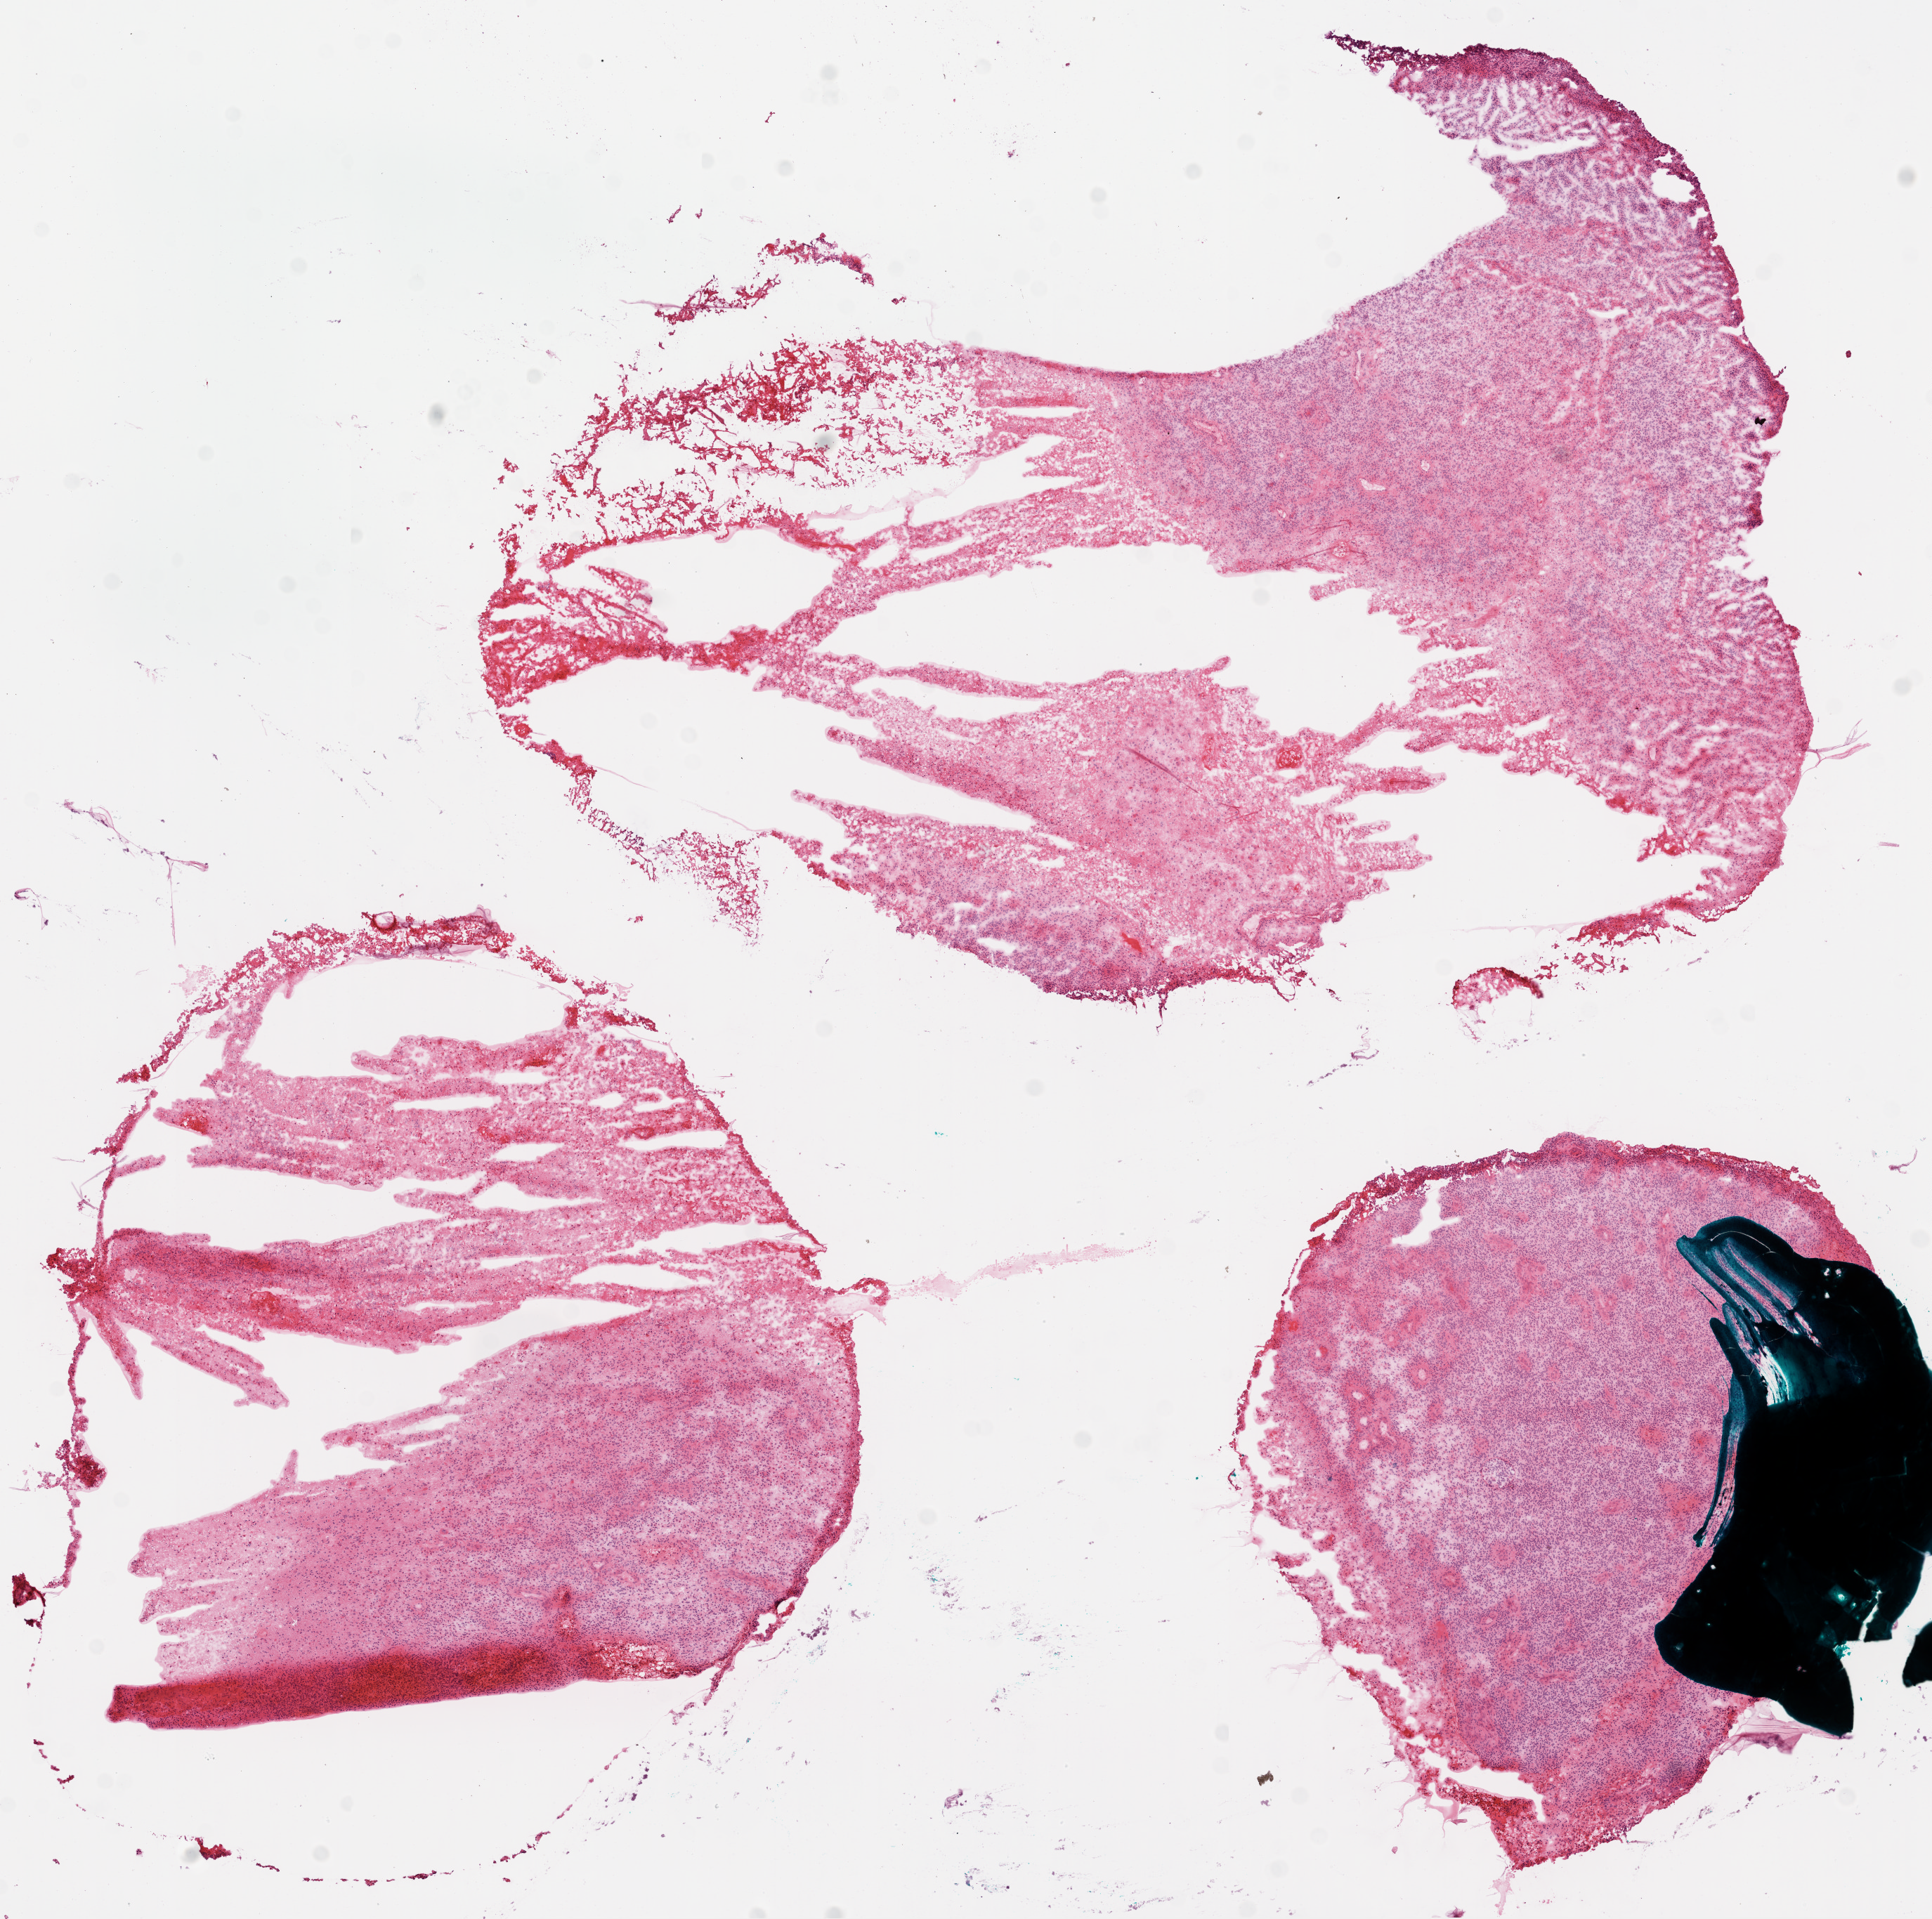
H&E-stained whole-slide image, low-resolution overview of the scanned area, about 11.0 x 11.0 mm. Frozen section from the bottom of the tissue portion. Sample: primary tumour, brain. Male patient; age at initial diagnosis 61 years. Pathologist review of this section (percent, as recorded): tumour cells 80%, tumour nuclei 100%, normal cells 0%, stromal cells 0%, necrosis 20%.
- histologic diagnosis: Glioblastoma